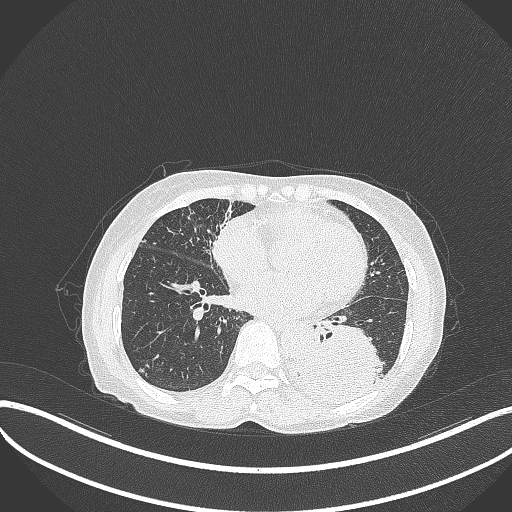
Chest CT, one axial slice. Slice 119 of 370 in the series (ordered by position). Reconstruction kernel B70f. 120 kVp. Lung window (W 1500 / L -600 HU). 1 mm slice thickness. 512 × 512 image matrix, field of view 400 × 400 mm. Female patient, age 78 years. From the clinical record (not read from this slice): clinical TNM (as recorded): T3 N0 M1.
Annotated regions visible in this slice (bounding box drawn by a radiologist):
- lung tumour (recorded histology: squamous cell carcinoma): bounding box <288,317,388,407> (left, top, right, bottom; pixels)